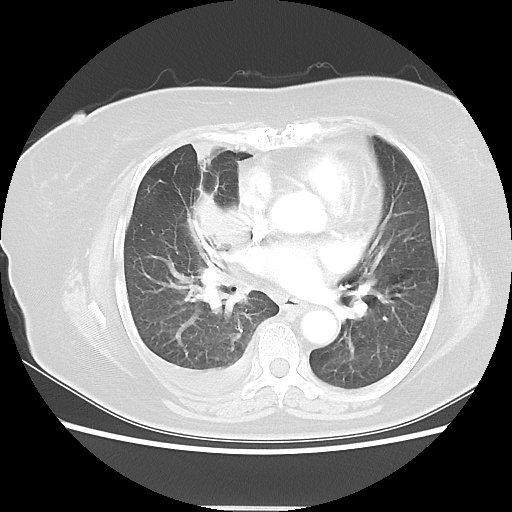
Chest CT, one axial slice. Slice 24 of 48 in the series (ordered by position). Lung window (W 1500 / L -600 HU). 5 mm slice thickness. 512 × 512 image matrix, field of view 360 × 360 mm. Patient: female, 73 years. Case-level facts recorded for this patient, not image findings: clinical TNM (as recorded): T3 N3 M1b; histopathological grade: G3.
Structures marked on this image (rectangle marked by the reading radiologist):
- lung tumour (recorded histology: small cell carcinoma): bounding box <175,179,260,321> (left, top, right, bottom; pixels)